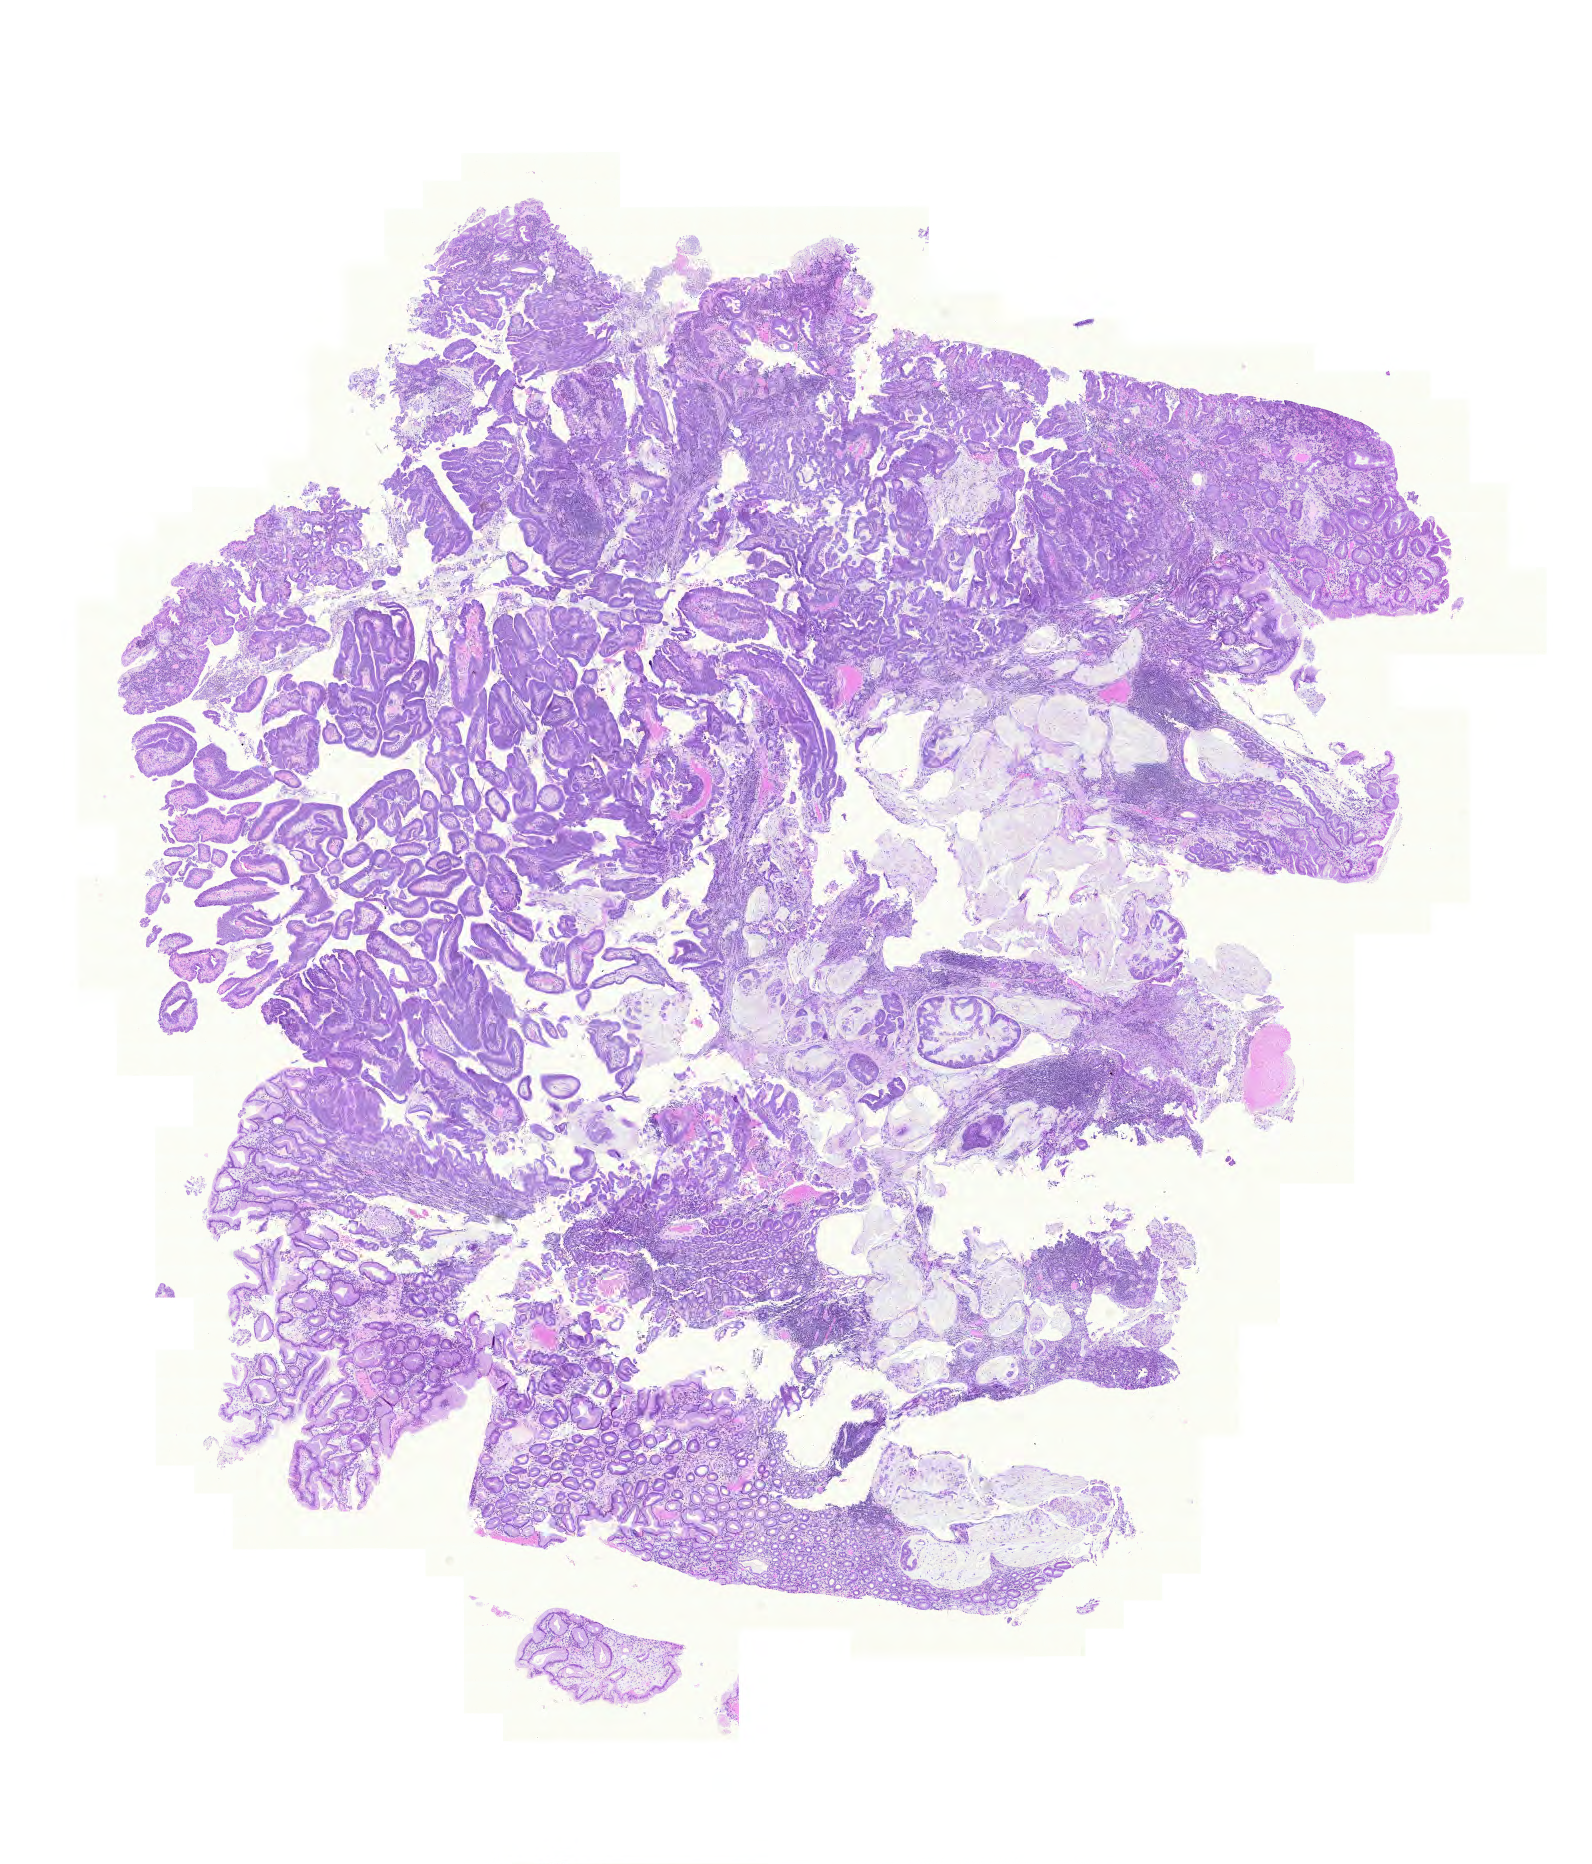
H&E-stained whole-slide image, low-resolution overview of the scanned area, about 11.8 x 13.9 mm, formalin-fixed paraffin-embedded (FFPE) diagnostic section, primary tumour sample from the stomach. Male patient.
Pathologic diagnosis: Adenocarcinoma, NOS (gastric antrum).